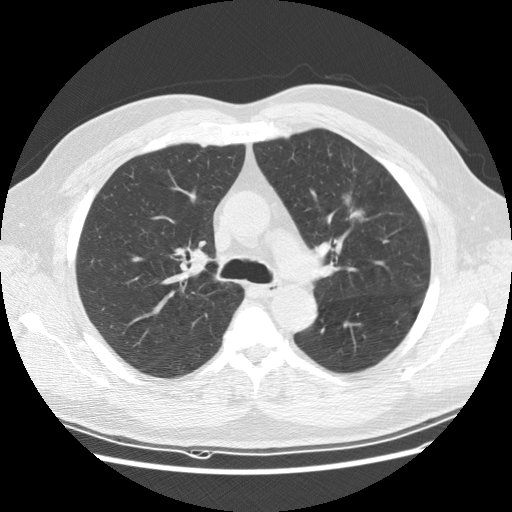
Axial slice from a low-dose chest CT screening exam, baseline annual screen, lung window (W 1500 / L -600 HU), slice 49 of 152 in the series. Male participant, aged 65 years at enrolment. Current smoker at enrolment.
- Expert reader's lesion annotation, box from (x=320, y=176) to (x=385, y=238) px.
- The screening reader recorded 2 non-calcified nodules or masses ≥4 mm on this exam (left upper lobe, right upper lobe); which of them this box marks is not recorded.
- Official screen result: positive, change unspecified: nodule(s) >= 4 mm or enlarging nodule(s), mass(es), or other non-specific abnormalities suspicious for lung cancer.
- Later outcome: lung cancer diagnosed 488 days after this screen — carcinoma, NOS, left upper lobe, poorly differentiated (G3), stage IIIA (AJCC 6th edition), 25 mm at pathology.